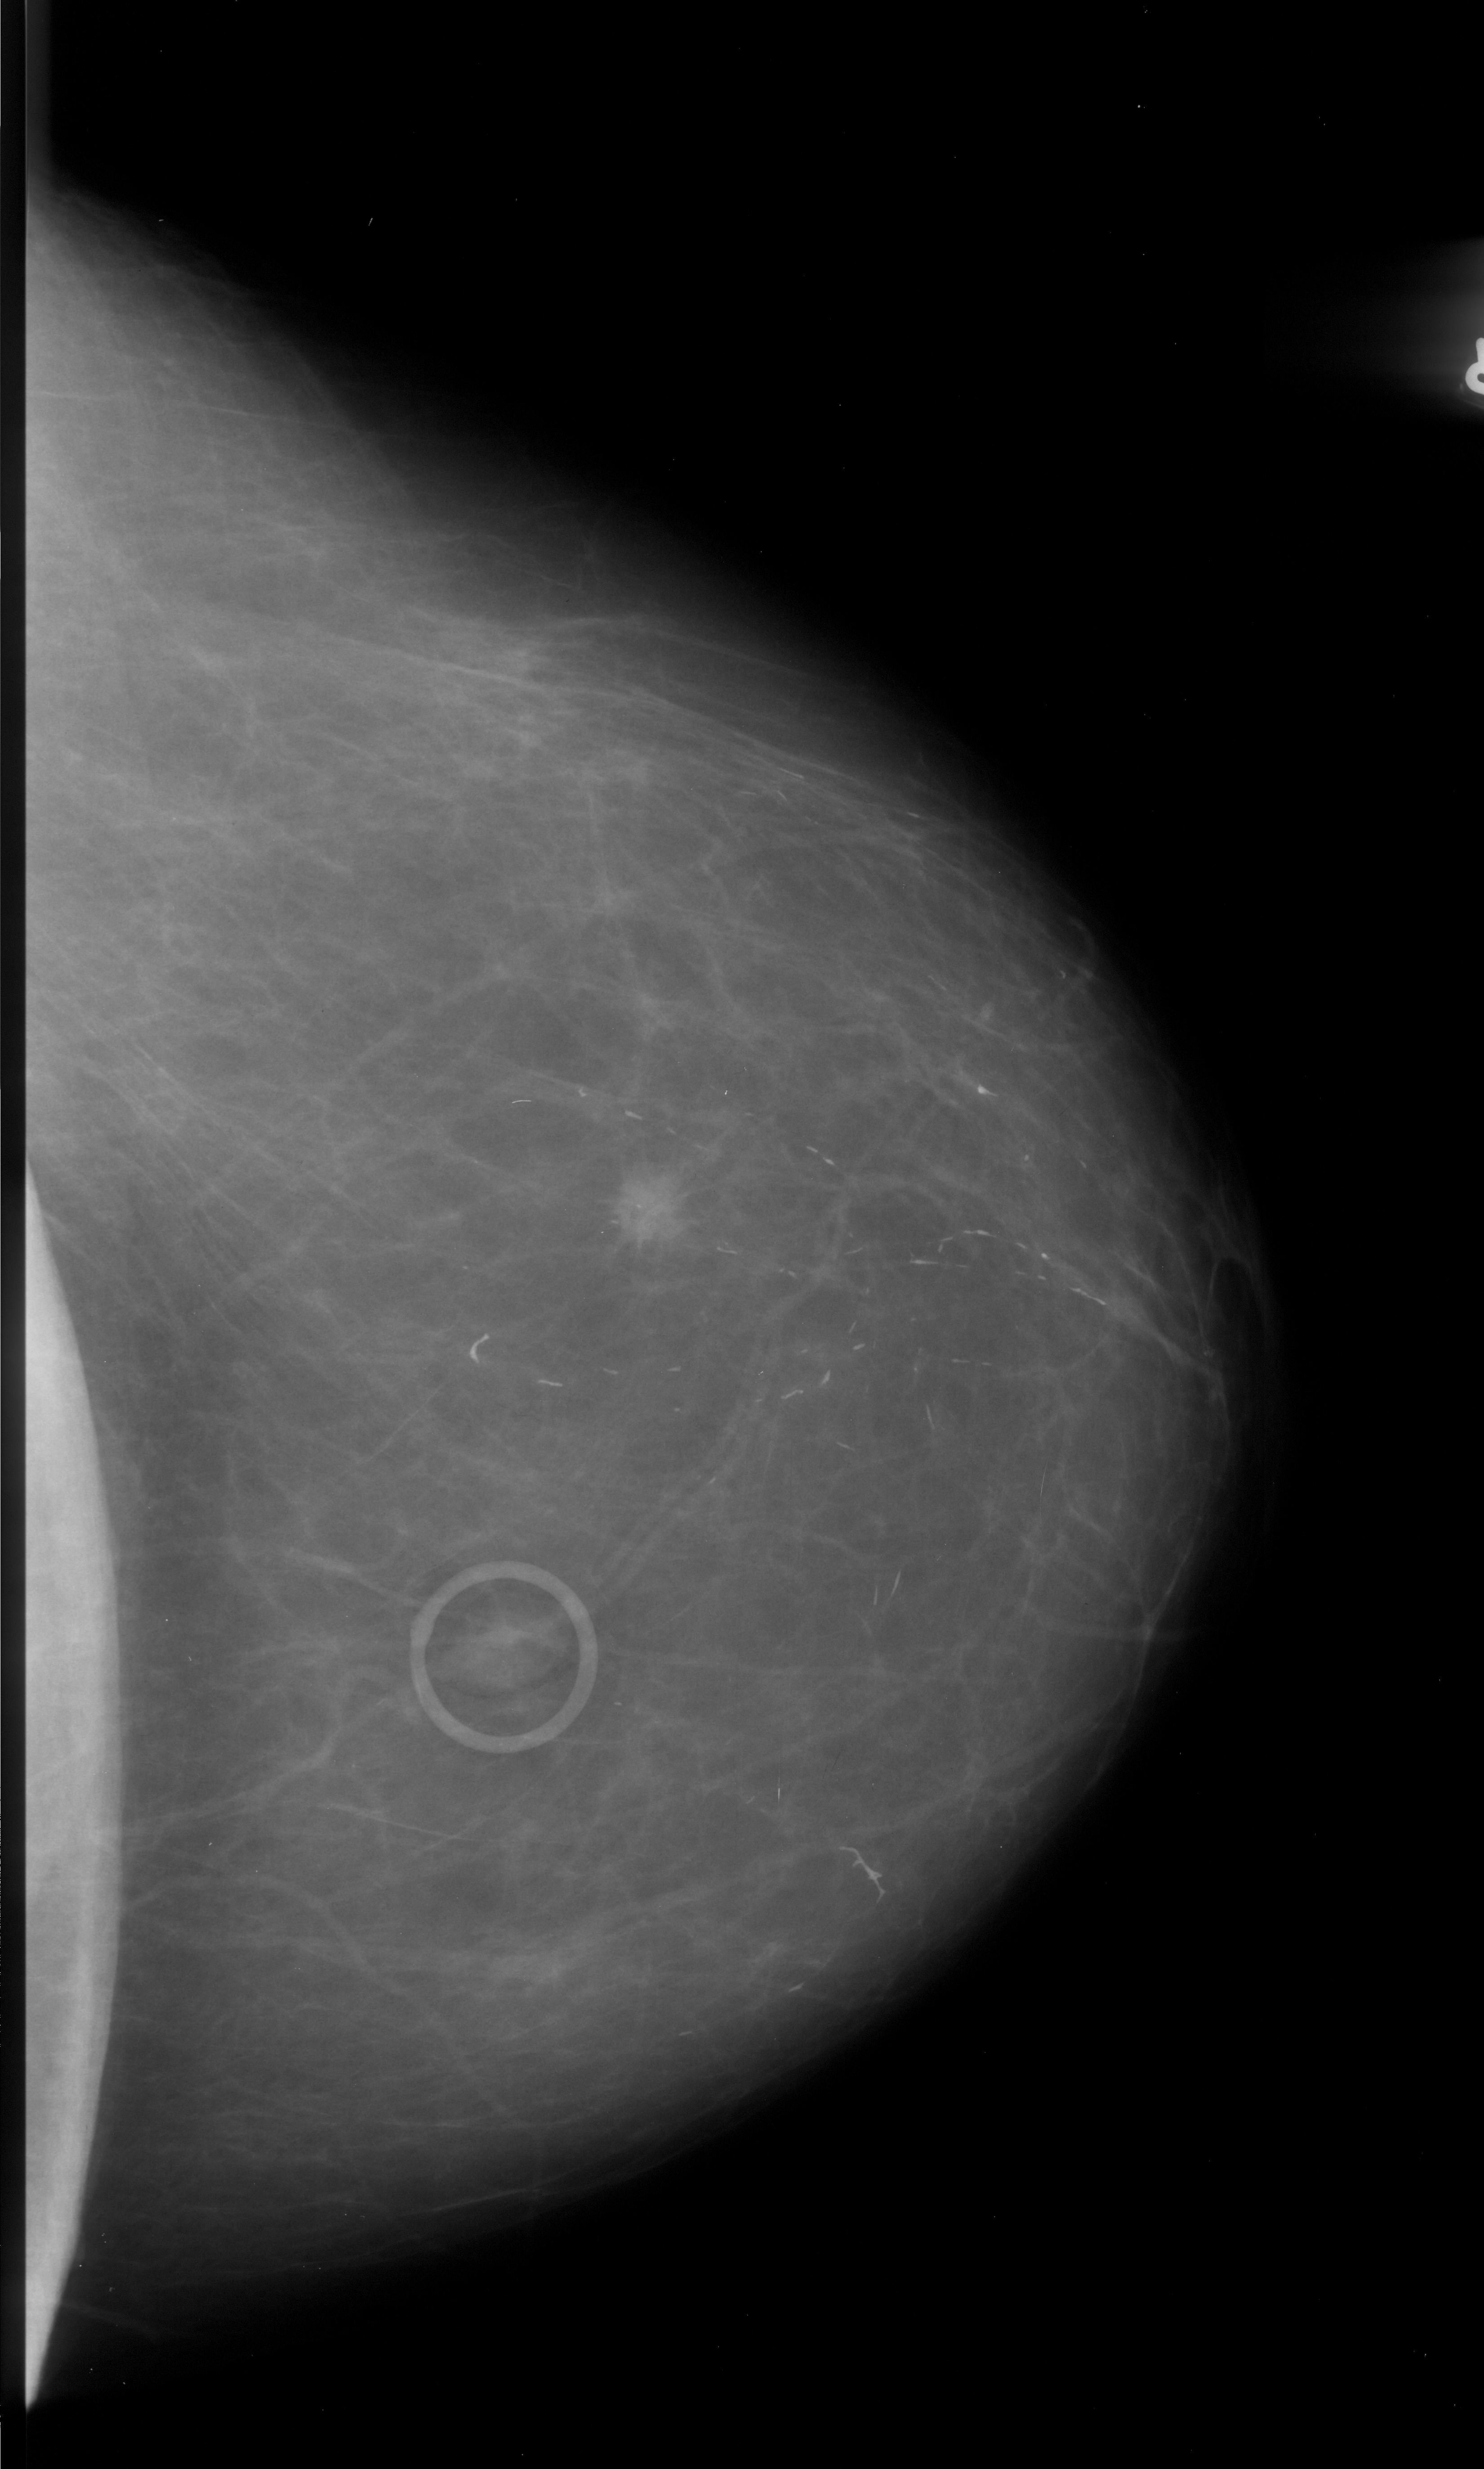
Digitized screen-film mammogram, right breast, CC view, breast composition: almost entirely fatty (BI-RADS density category 1 of 4).
Radiologist-marked abnormalities on this image: mass, shape irregular, margins spiculated; BI-RADS assessment category 5; pathology (as recorded): malignant.